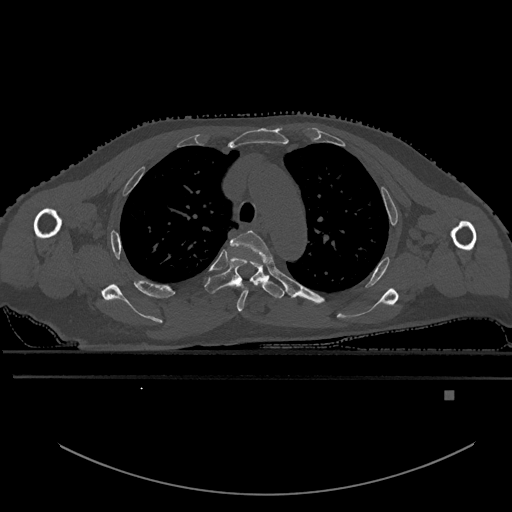
CT including the spine, one axial slice; position 423 of 969 along the scan axis; bone window (W 1800 / L 400 HU); 0.5 mm slice thickness; 512 × 512 image matrix. Patient: male, 82 years. From the clinical record (not read from this slice): primary cancer: prostate.
Annotated regions visible in this slice (semi-automatically segmented with operator editing):
- T3 vertebra: bounding box [x1, y1, x2, y2] px = [231, 230, 273, 312]
- T4 vertebra: [204, 256, 285, 299]